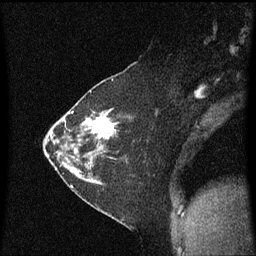
Breast MRI (dynamic contrast-enhanced), one sagittal slice. Slice 35 of 60 in the series (ordered by position). Dynamic contrast-enhanced series, image 2 of 3 at this slice position (ordered by acquisition). 1.5 T. TE 4.2 ms, TR 8.4 ms. 2 mm slice thickness. 256 × 256 image matrix, field of view 200 × 200 mm. Patient: female, 36 years. Case-level facts recorded for this patient, not image findings: setting: breast cancer imaged before/during neoadjuvant chemotherapy; receptor status: HR-positive, HER2-negative.
Structures marked on this image (semi-automatic segmentation, software-assisted and operator-edited):
- analysis volume of interest (the breast-tissue region the enhancement analysis was run in; not a lesion): bounding box [x1, y1, x2, y2] px = [66, 102, 119, 179]
- tumour enhancement mask (voxels above the 70 % enhancement threshold inside the analysis volume of interest): [83, 110, 117, 139]